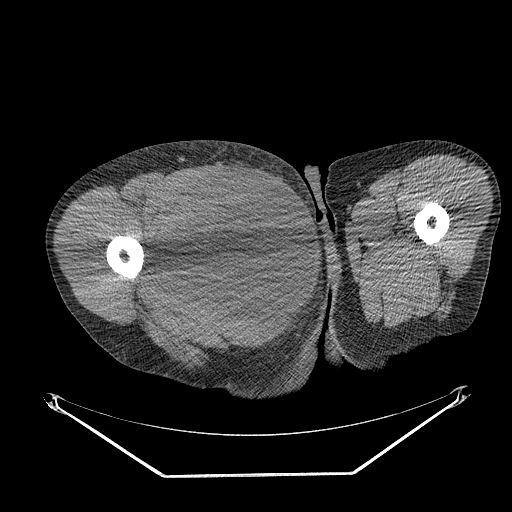
CT of an extremity soft-tissue mass (from a PET/CT study), one axial slice; position 267 of 311 along the scan axis; soft-tissue window (W 400 / L 40 HU); 512 × 512 image matrix, field of view 500 × 500 mm. Male patient. Case-level facts recorded for this patient, not image findings: histological type: undifferentiated - pleiomorphic; grade: high; site of the primary tumour: right thigh.
Outlined on this slice (expert contour drawn on MRI and transferred to this co-registered scan by the dataset authors):
- gross tumour volume including surrounding oedema: bounding box (x1, y1, x2, y2) in pixels: (155, 171, 268, 279)
- gross tumour volume (mass): (158, 171, 268, 279)